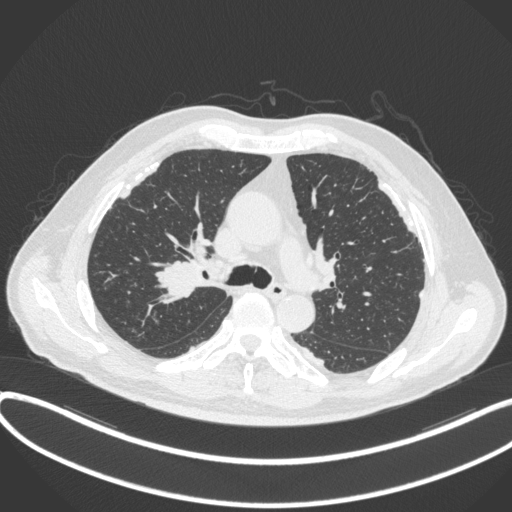
Chest CT, one axial slice. Slice 279 of 455 in the series (ordered by position). Lung window (W 1500 / L -600 HU). 1 mm slice thickness. 512 × 512 image matrix, field of view 400 × 400 mm. Patient: male, 58 years. Case-level facts recorded for this patient, not image findings: clinical TNM (as recorded): T1c N0 M0.
Structures marked on this image (bounding box drawn by a radiologist):
- lung tumour (recorded histology: squamous cell carcinoma): box from (x=148, y=250) to (x=201, y=303) px